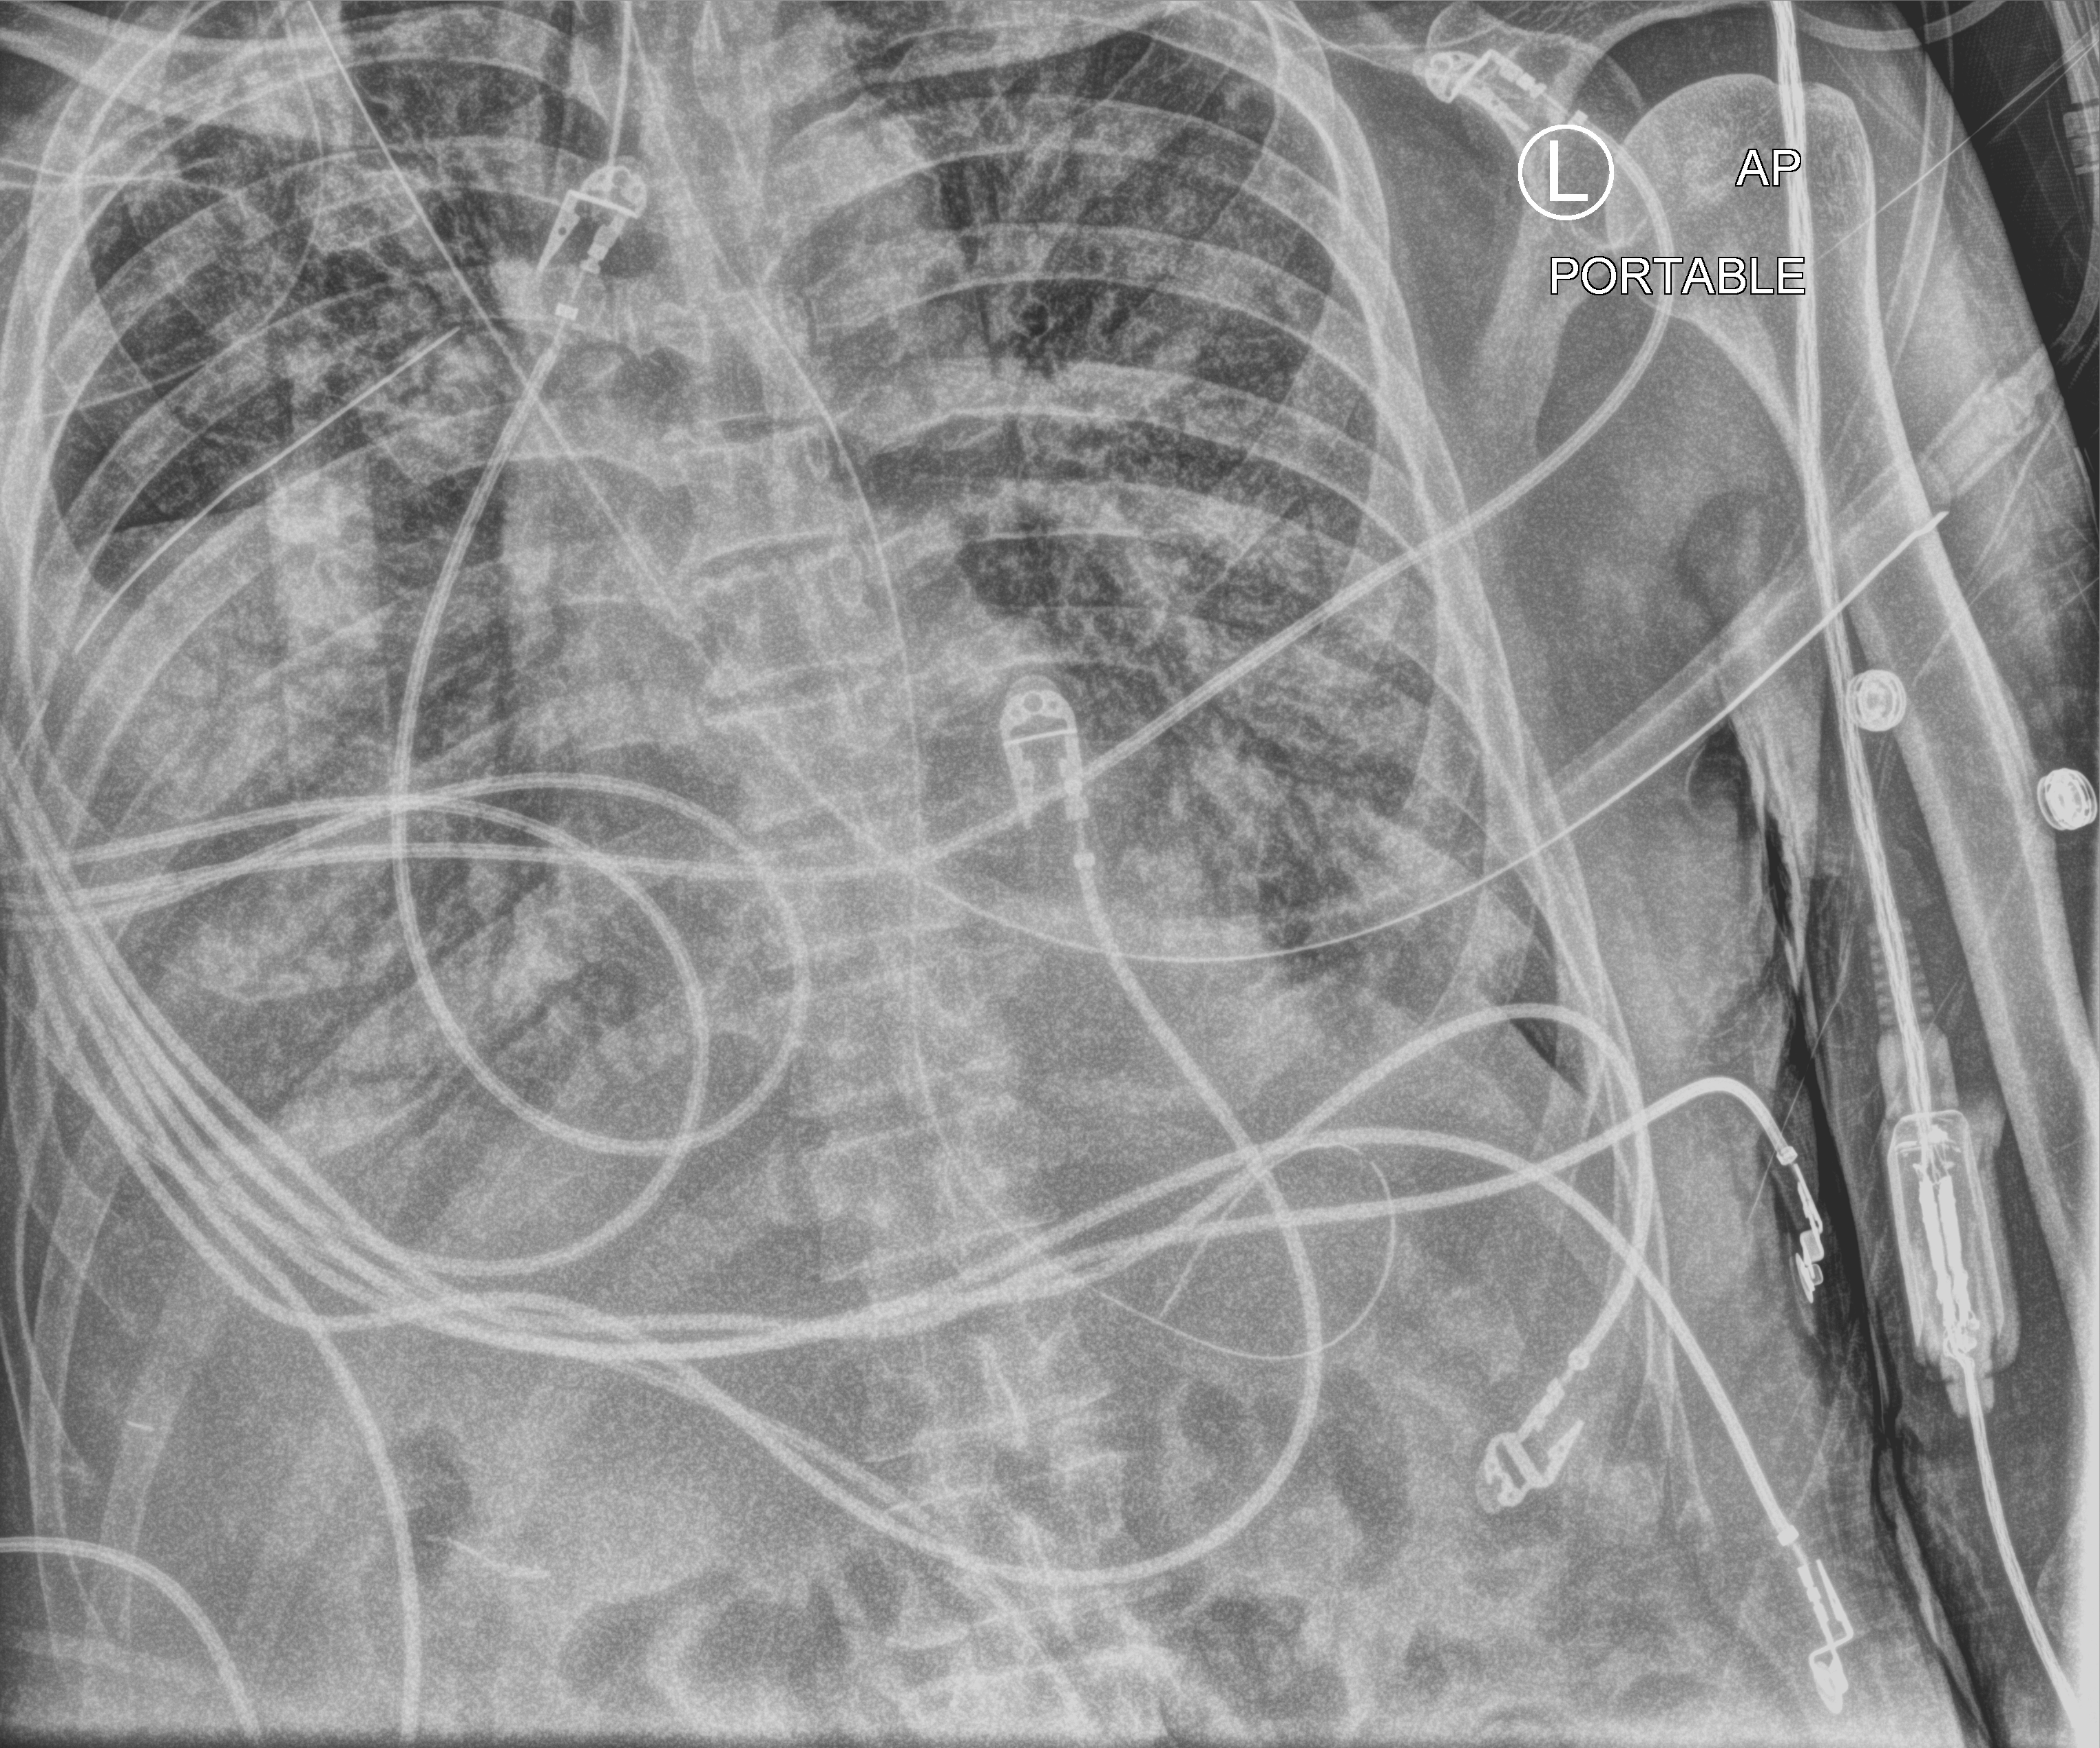
Bedside chest radiograph (computed radiography). Male patient hospitalised with COVID-19, age 60–74 years.
Hospital-stay facts (about this admission, not read from this image; timing relative to this image not recorded): smoking status (admission record): former.